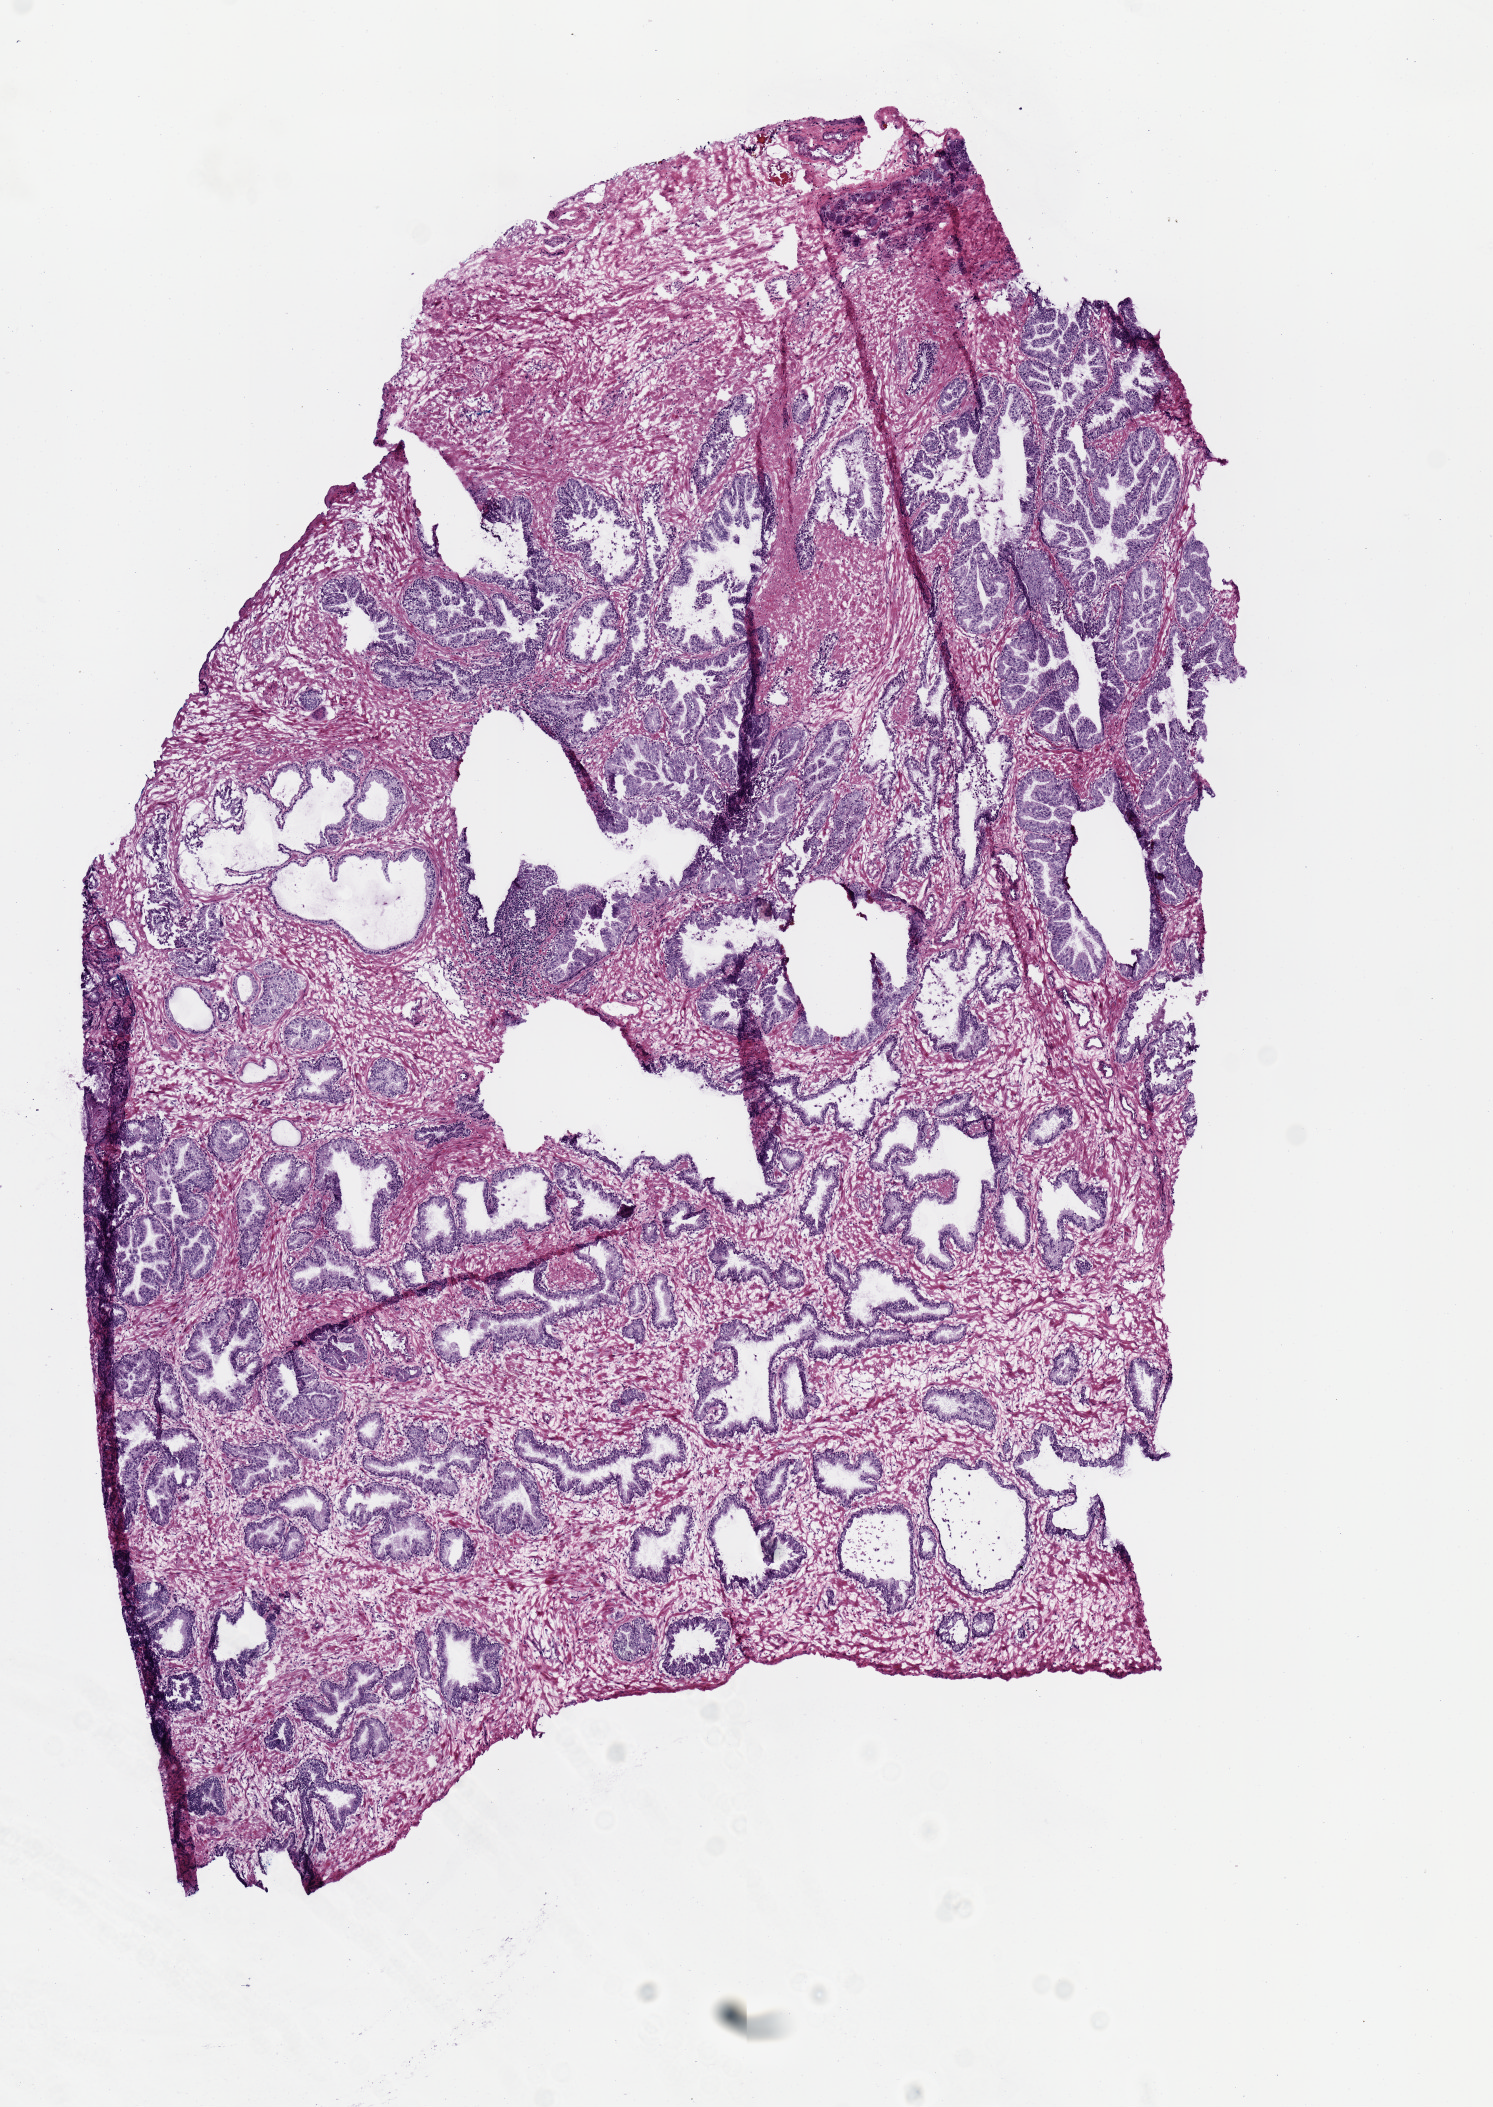
Whole-slide histology image, H&E-stained, shown as a low-resolution overview of the whole scanned area (about 5.9 x 8.3 mm, from a 20x scan). Frozen section from the top of the tissue portion. Sample: primary tumour, prostate. Male, age 50 years at initial diagnosis.
Pathologic diagnosis: Acinar cell carcinoma (prostate gland).